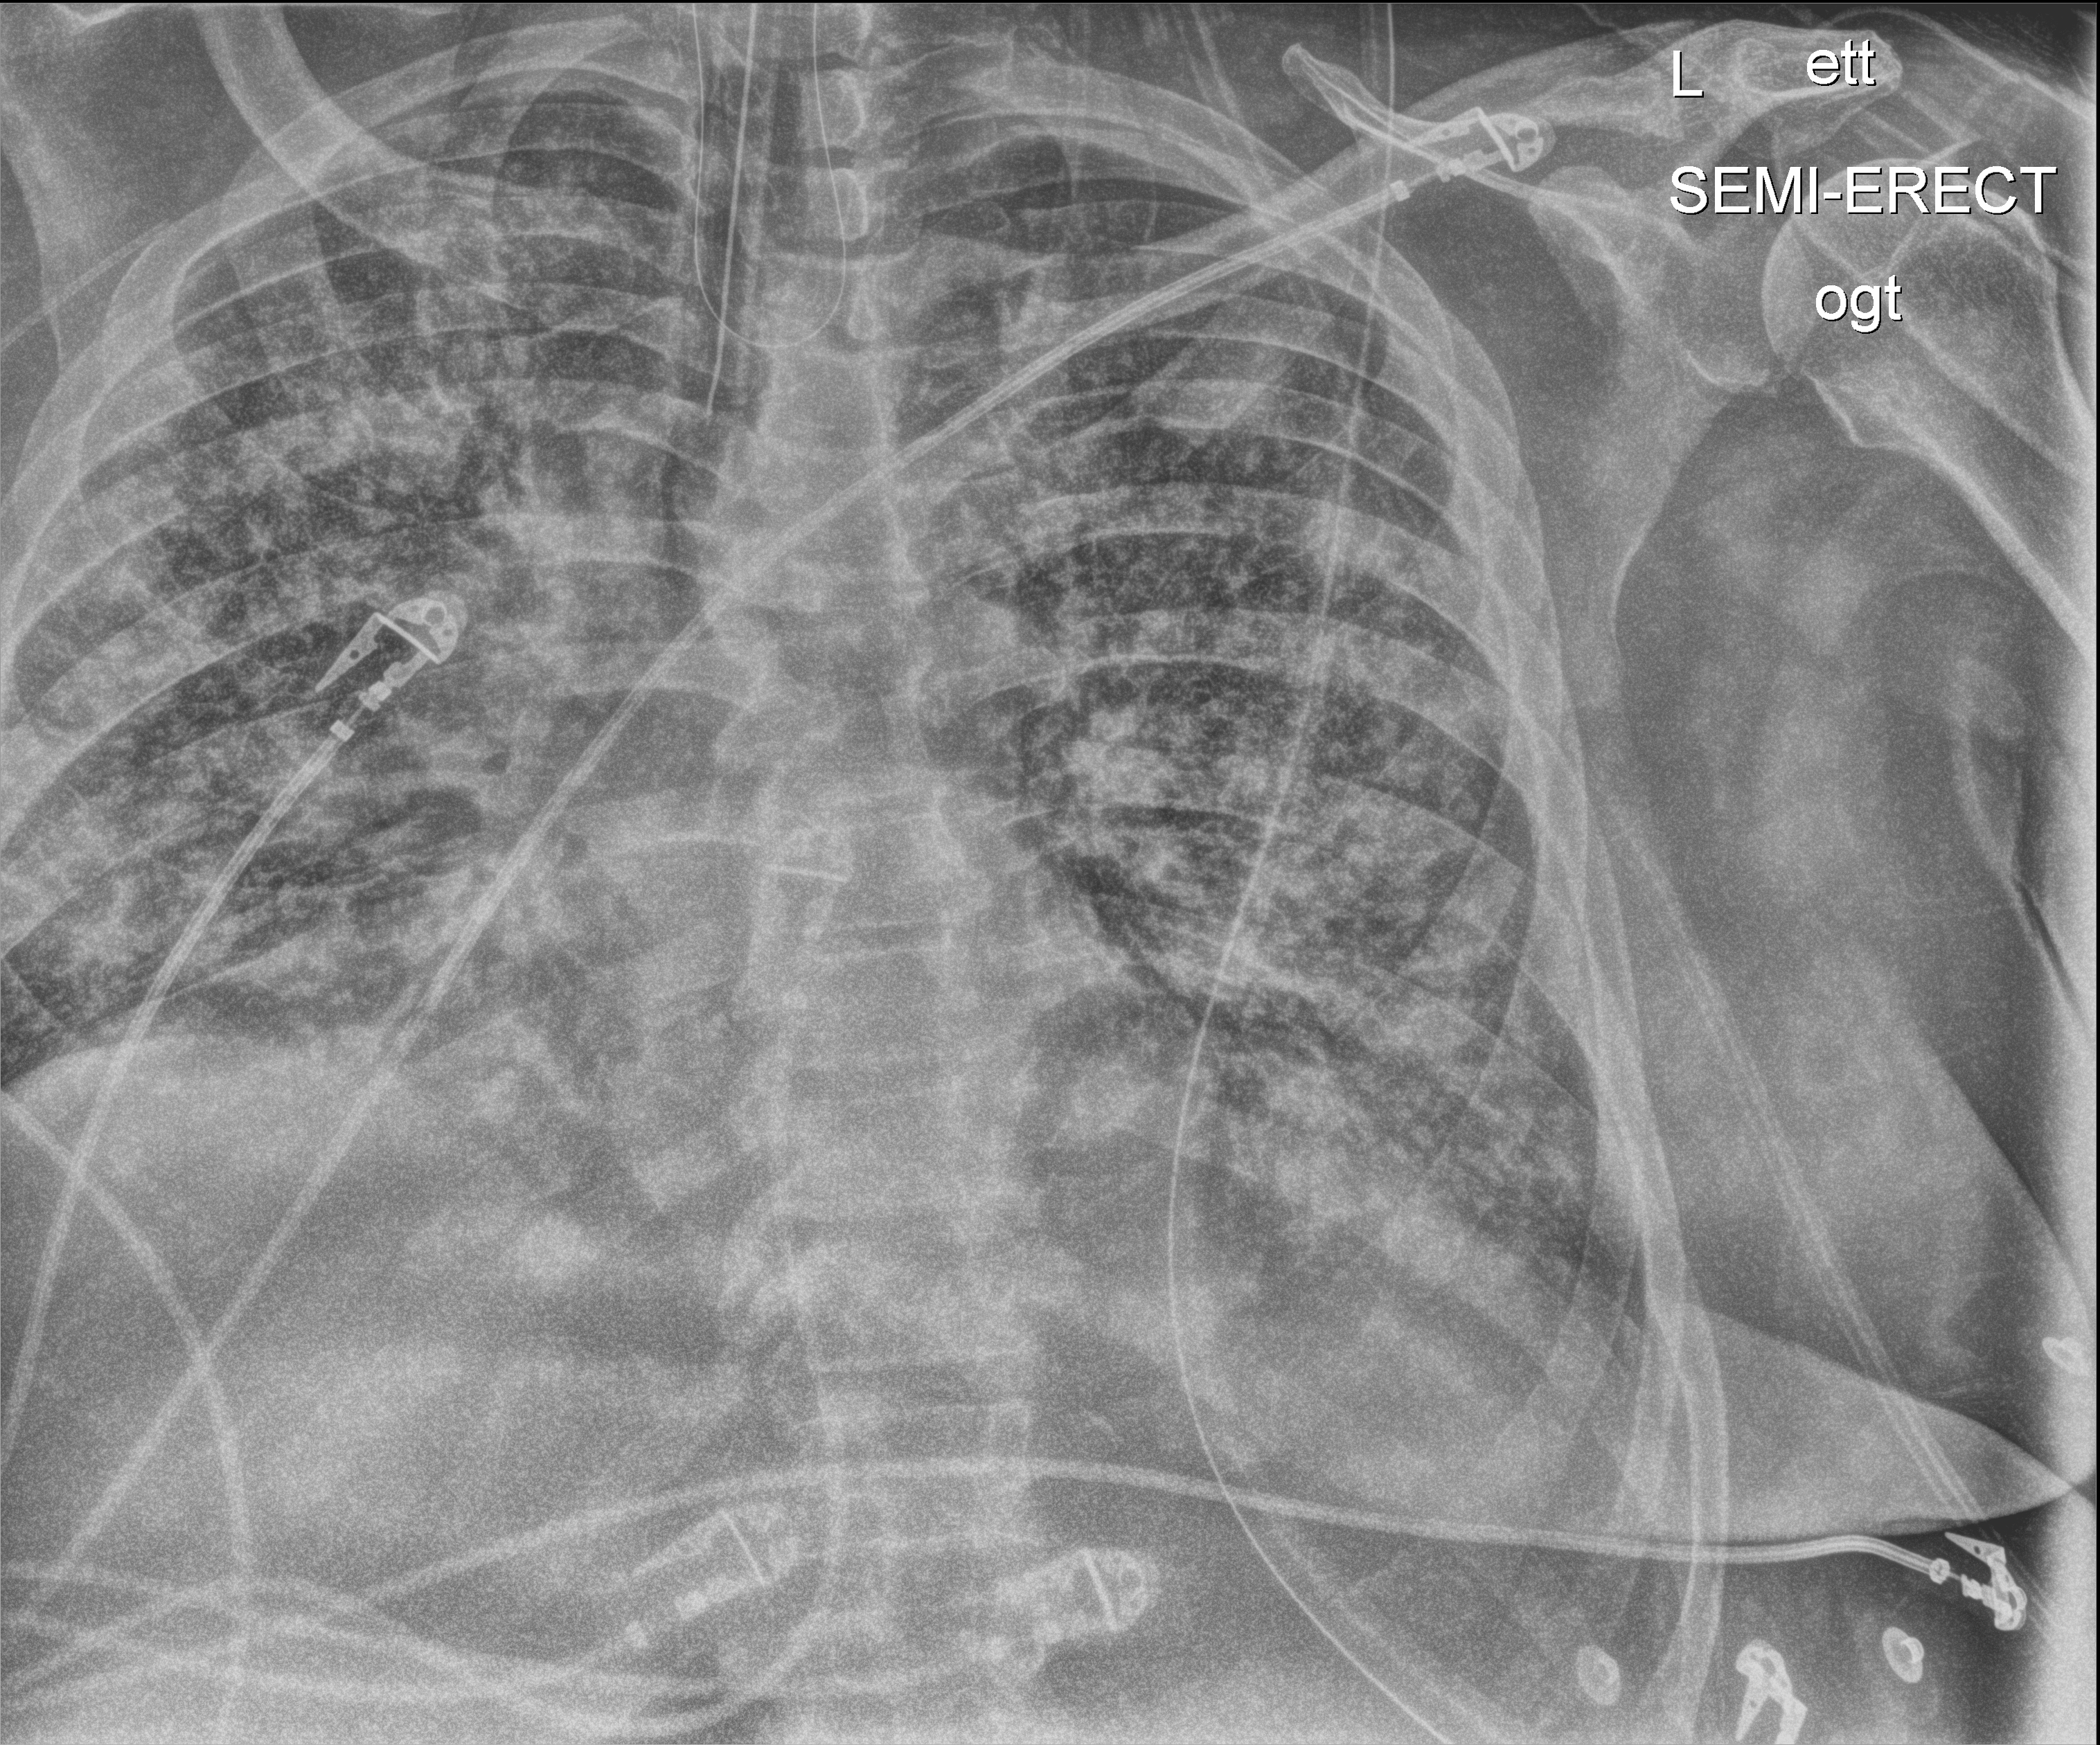
Chest X-ray (portable). Patient hospitalised with COVID-19; male, aged 60–74 years.
From the hospital-stay record, not from the radiograph (when in the stay this image was taken is not recorded): length of hospital stay: 34 days.